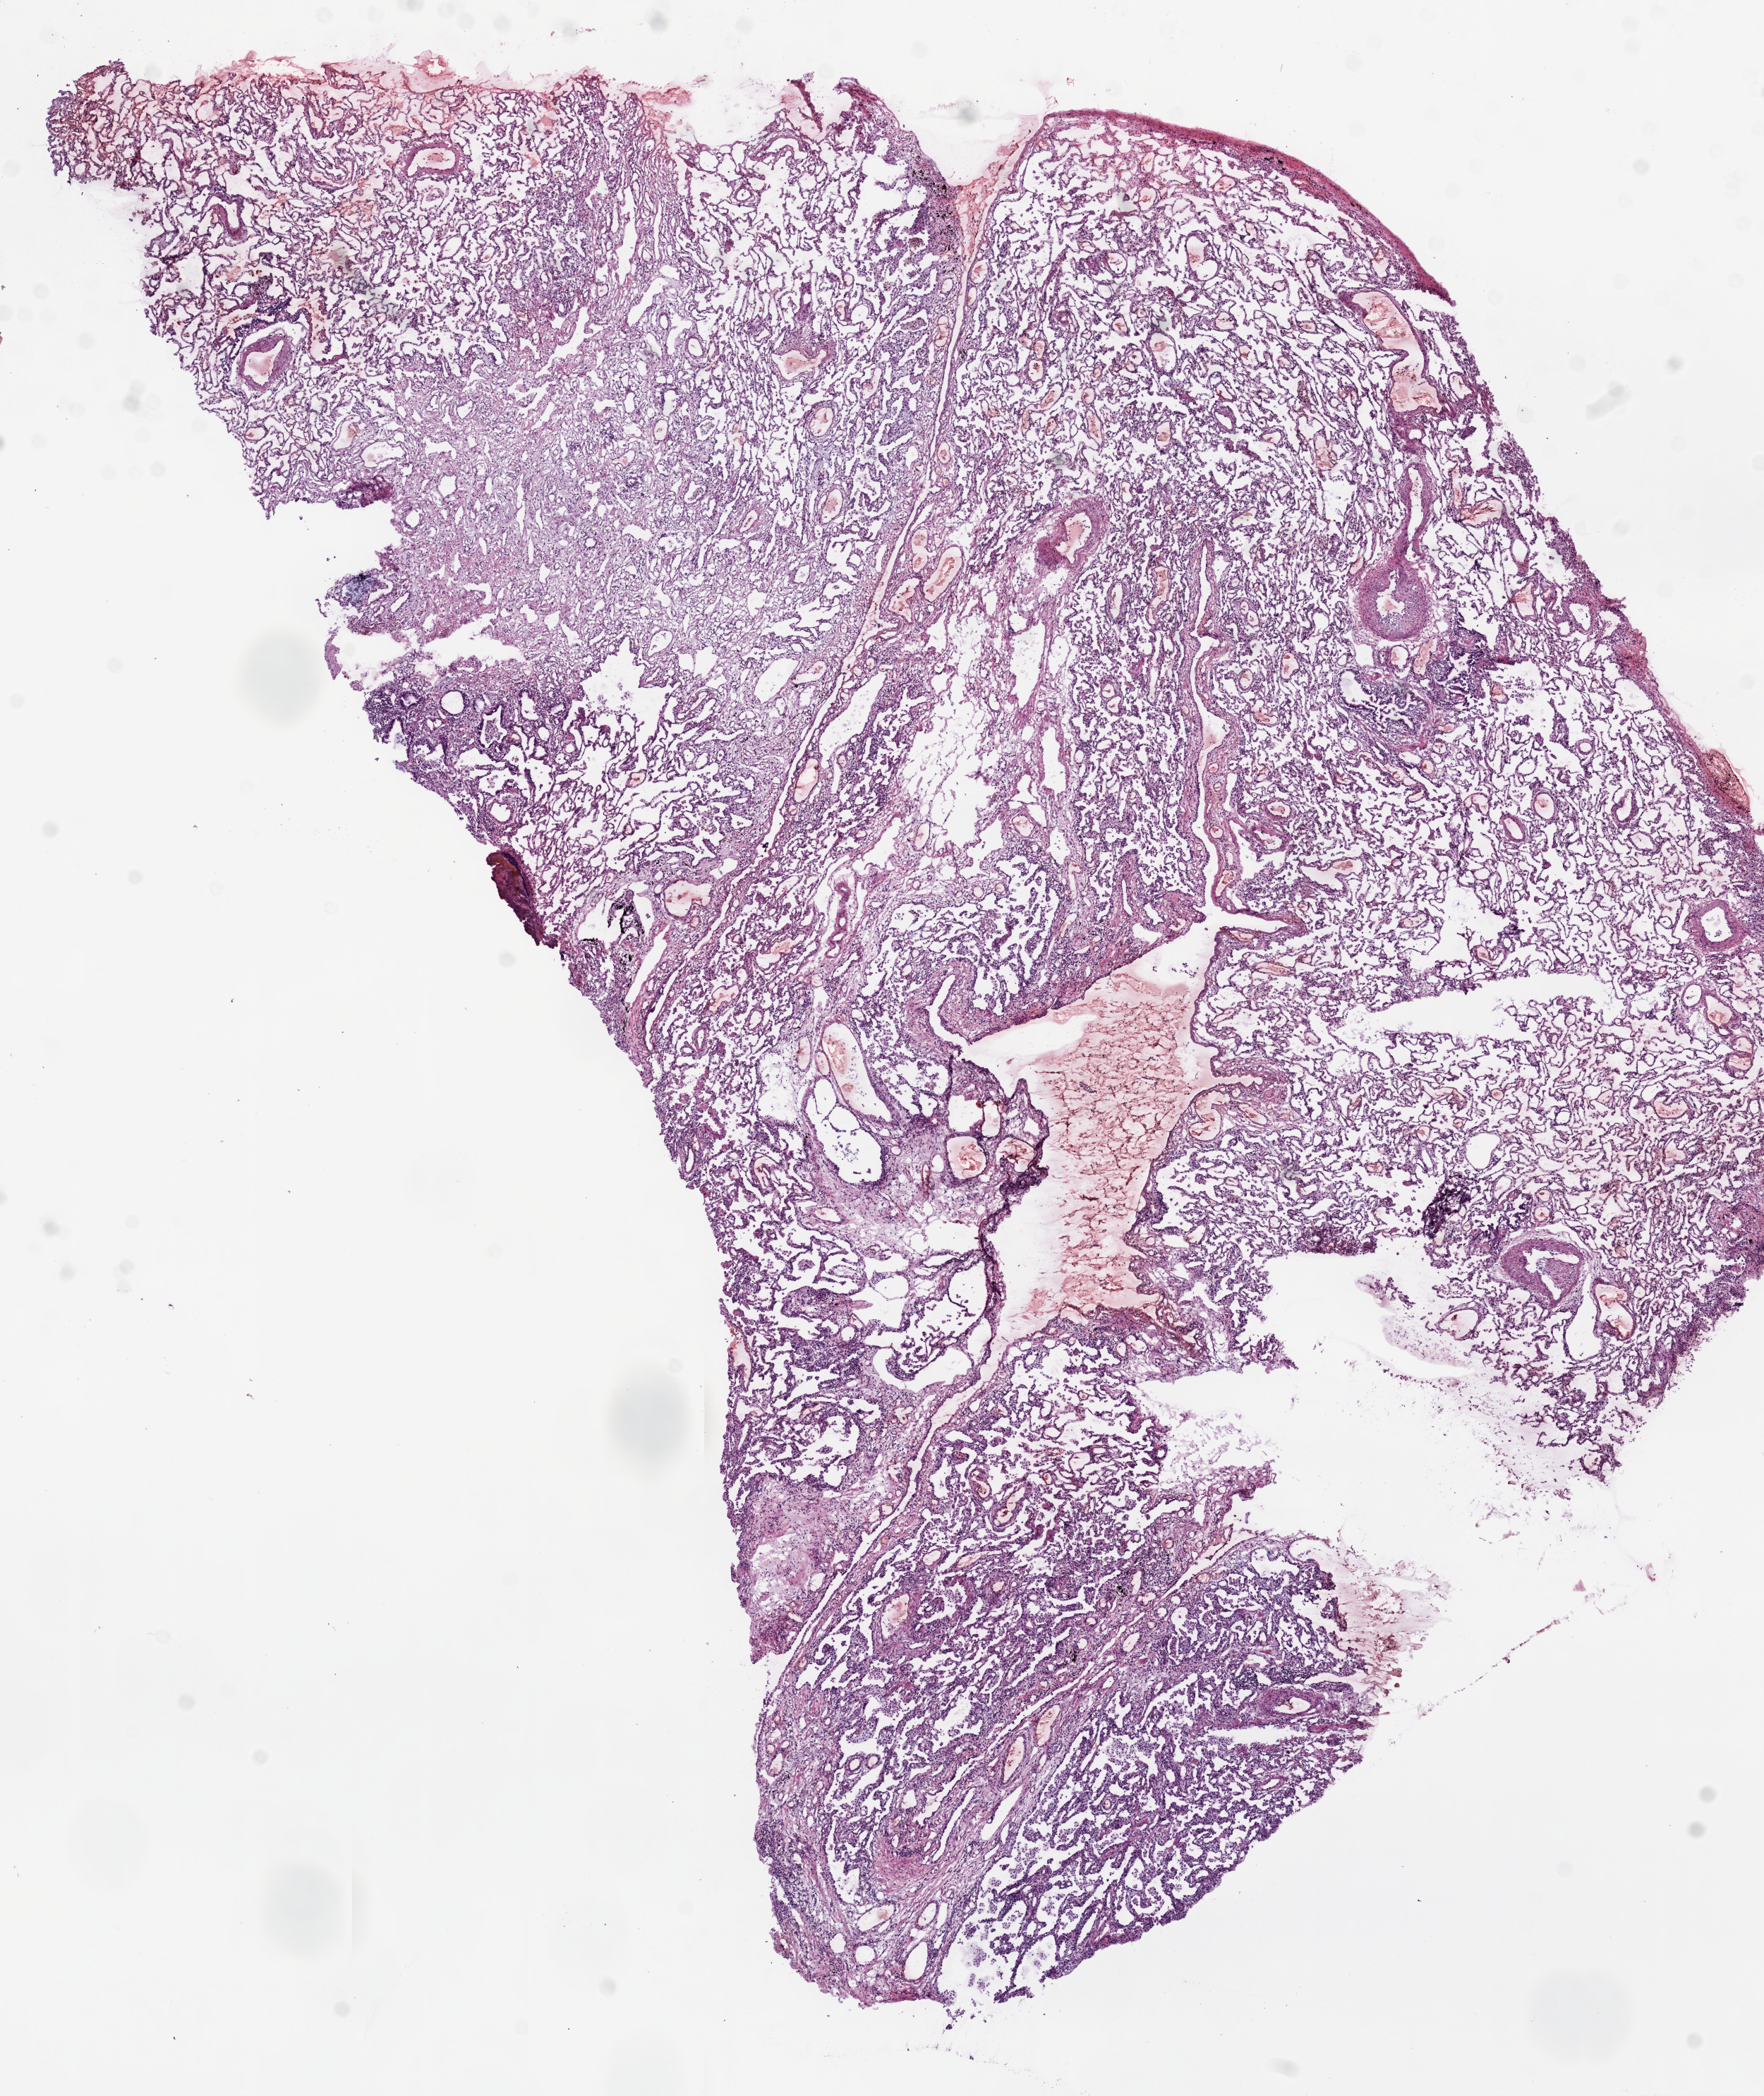
H&E whole-slide image — low-resolution overview of the scanned area, about 10.0 x 11.9 mm (from a 20x scan). Frozen section from the top of the tissue portion. Solid tissue normal (non-tumour tissue) sample from the lung. Female, age 62 years at initial diagnosis.
This section: solid tissue normal (non-tumour) sample from the same patient. Patient diagnosis: Squamous cell carcinoma, NOS.